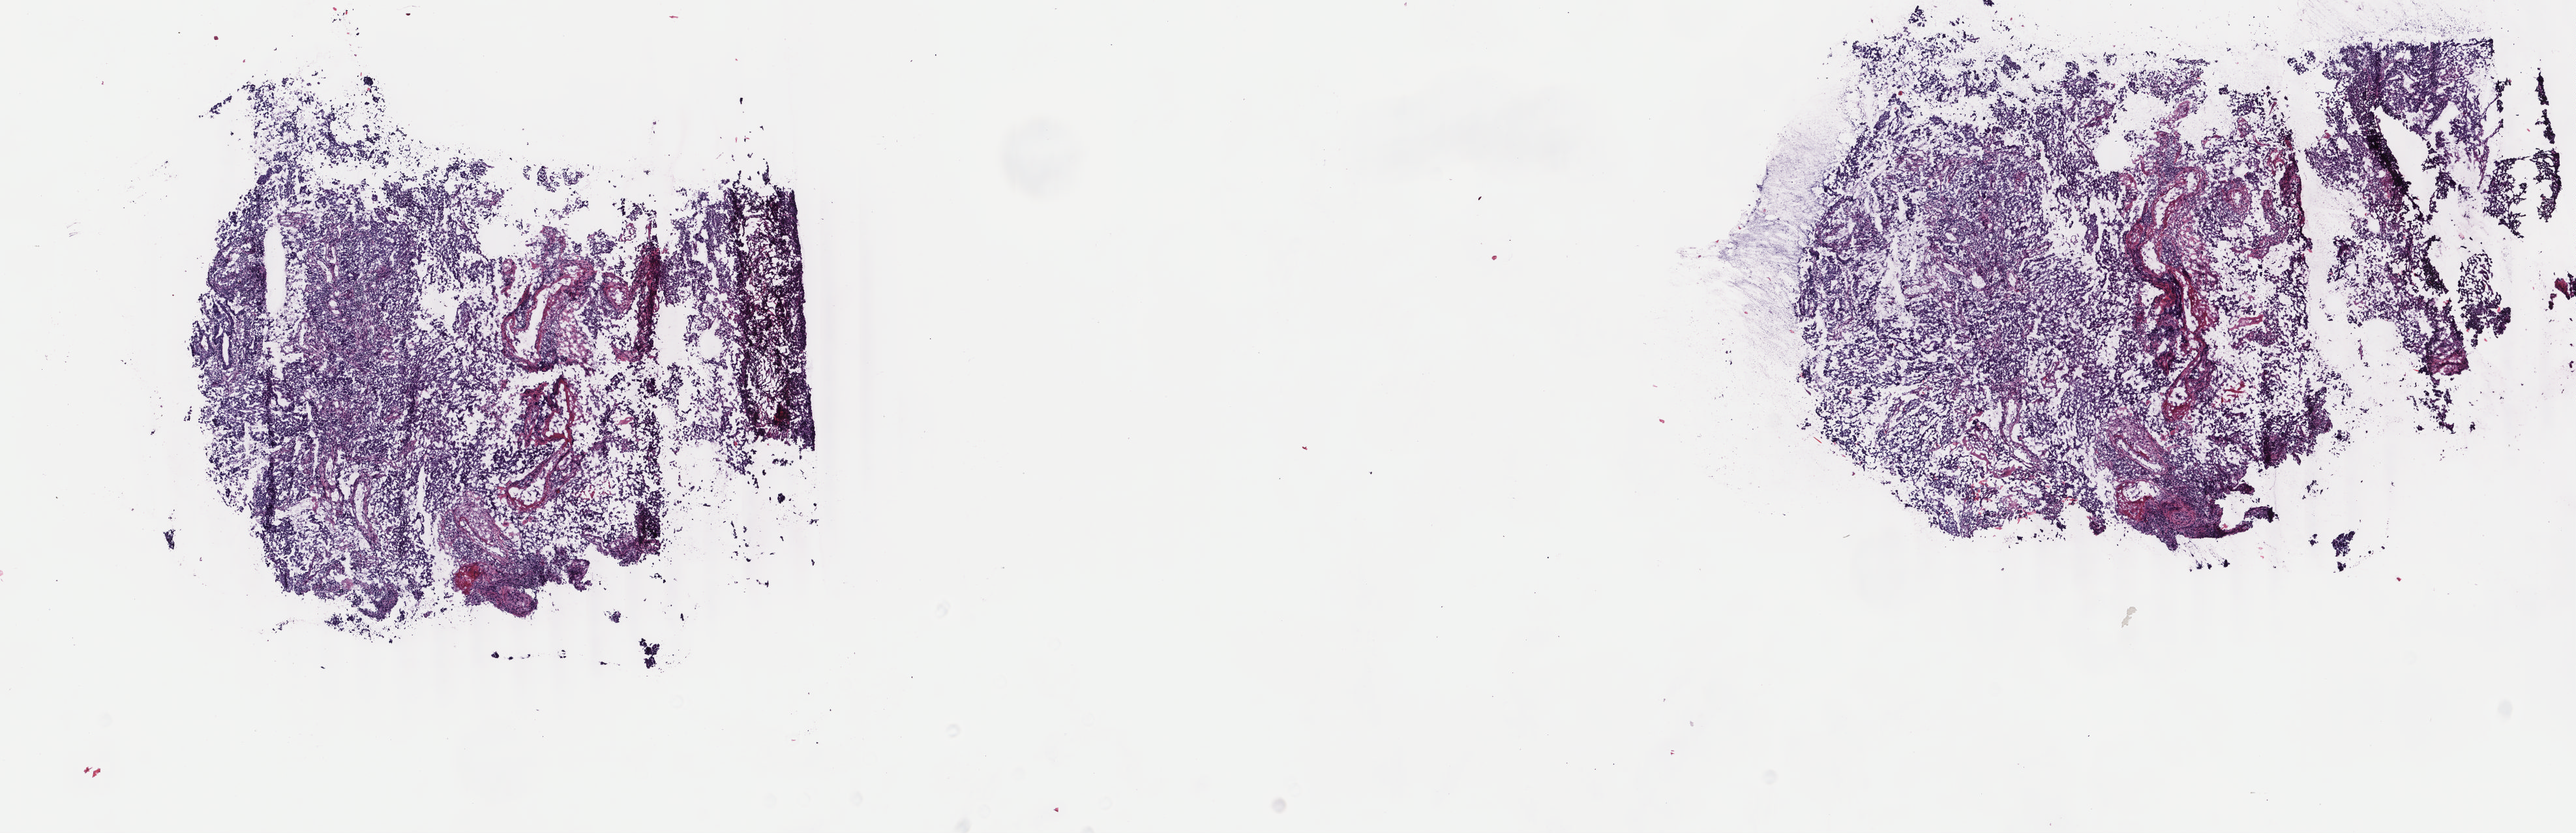
Whole-slide histology image, H&E-stained, a low-resolution overview of the entire scanned area, about 15.7 x 5.1 mm (from a 40x scan); frozen section from the top of the tissue portion; primary tumour sample from the uterus. Female, age 46 years at initial diagnosis. Pathologist review of this section (percent, as recorded): tumour cells 100%, tumour nuclei 90%.
Pathologic diagnosis: Endometrioid adenocarcinoma, NOS (endometrium).